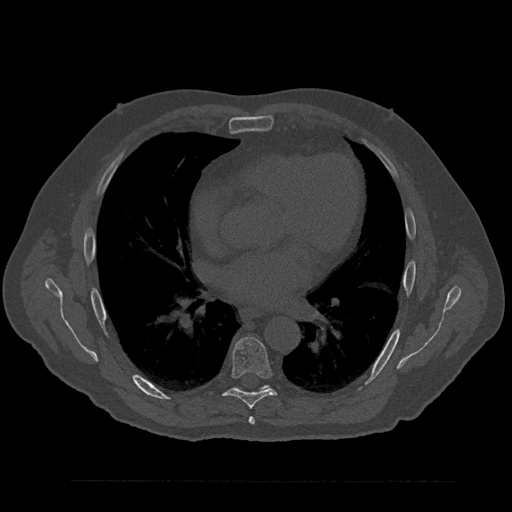
CT including the spine, one axial slice; reconstruction kernel Br40s/3; 120 kVp; bone window (W 1800 / L 400 HU); 512 × 512 image matrix, field of view 430 × 430 mm. Patient: male, 61 years. Case-level facts recorded for this patient, not image findings: primary cancer: prostate.
Outlined on this slice (semi-automatic segmentation, software-assisted and operator-edited):
- T6 vertebra: bounding box <249,416,255,425> (left, top, right, bottom; pixels)
- T7 vertebra: <208,337,276,409>
- T8 vertebra: <234,386,269,389>